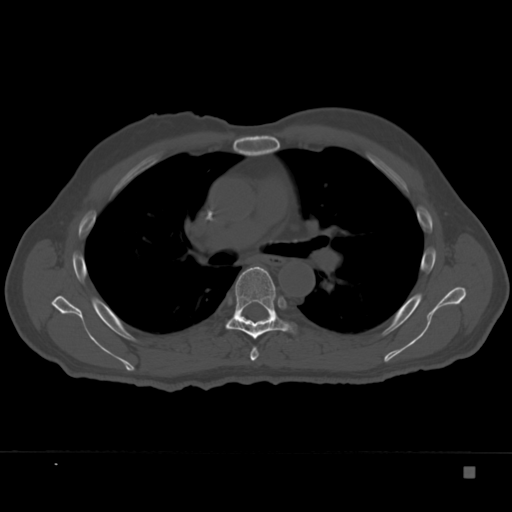
CT including the spine, one axial slice; slice 242 of 332 in the series (ordered by position); reconstruction kernel Br40s; bone window (W 1800 / L 400 HU); 1.5 mm slice thickness; 512 × 512 image matrix, field of view 389 × 389 mm. Patient: male, 72 years. Case-level facts recorded for this patient, not image findings: primary cancer: skeletal.
Outlined on this slice (semi-automatic segmentation, software-assisted and operator-edited):
- T5 vertebra: bounding box (x1, y1, x2, y2) in pixels: (250, 347, 259, 361)
- T6 vertebra: (217, 267, 298, 339)